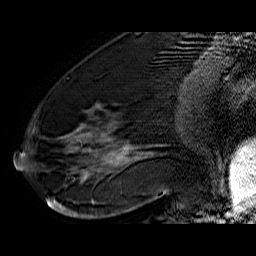
Breast MRI (dynamic contrast-enhanced), one sagittal slice. Slice 24 of 60 in the series (ordered by position). Dynamic contrast-enhanced series, time point 2 of 6 at this slice position (early post-contrast). 1.5 T. TE 6.4 ms, TR 32.9 ms. 256 × 256 image matrix, field of view 200 × 200 mm. Female patient. Case-level facts recorded for this patient, not image findings: setting: breast cancer imaged before/during neoadjuvant chemotherapy; receptor status: HR-positive, HER2-negative.
Outlined on this slice (semi-automatic segmentation, software-assisted and operator-edited):
- analysis volume of interest (the breast-tissue region the enhancement analysis was run in; not a lesion): bounding box <42,74,176,210> (left, top, right, bottom; pixels)
- tumour enhancement mask (voxels above the 100 % enhancement threshold inside the analysis volume of interest): <47,107,137,210>